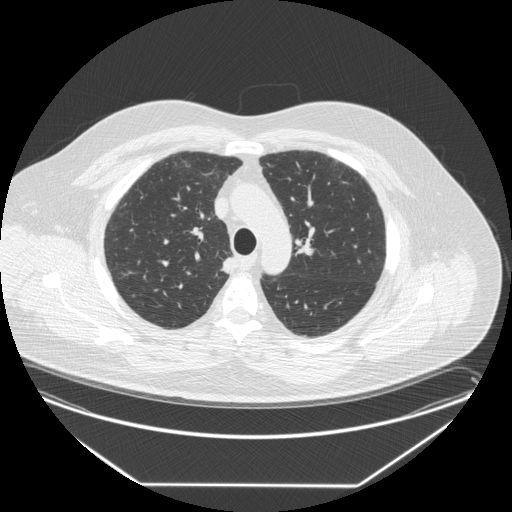
Axial slice from a low-dose chest CT screening exam, third annual screen, lung window (W 1500 / L -600 HU), 2.5 mm slice thickness, standard (soft-tissue) reconstruction kernel (STANDARD), slice 60 of 258 in the series. Male participant, aged 58 years at enrolment. Former smoker at enrolment.
Lesion marked by an expert reader, bounding box [x1, y1, x2, y2] px = [213, 253, 244, 280]. The exam's reader record, not a measurement of the box and not confirmed to be the same lesion: non-calcified nodule or mass ≥4 mm, right upper lobe, 15 × 12 mm, smooth margins, soft tissue attenuation, pre-existing on the prior screen: no. Official screen result: positive, other. Later outcome: lung cancer diagnosed 17 days after this screen — large cell carcinoma, NOS, right upper lobe, stage IV (AJCC 6th edition), 35 mm at pathology.